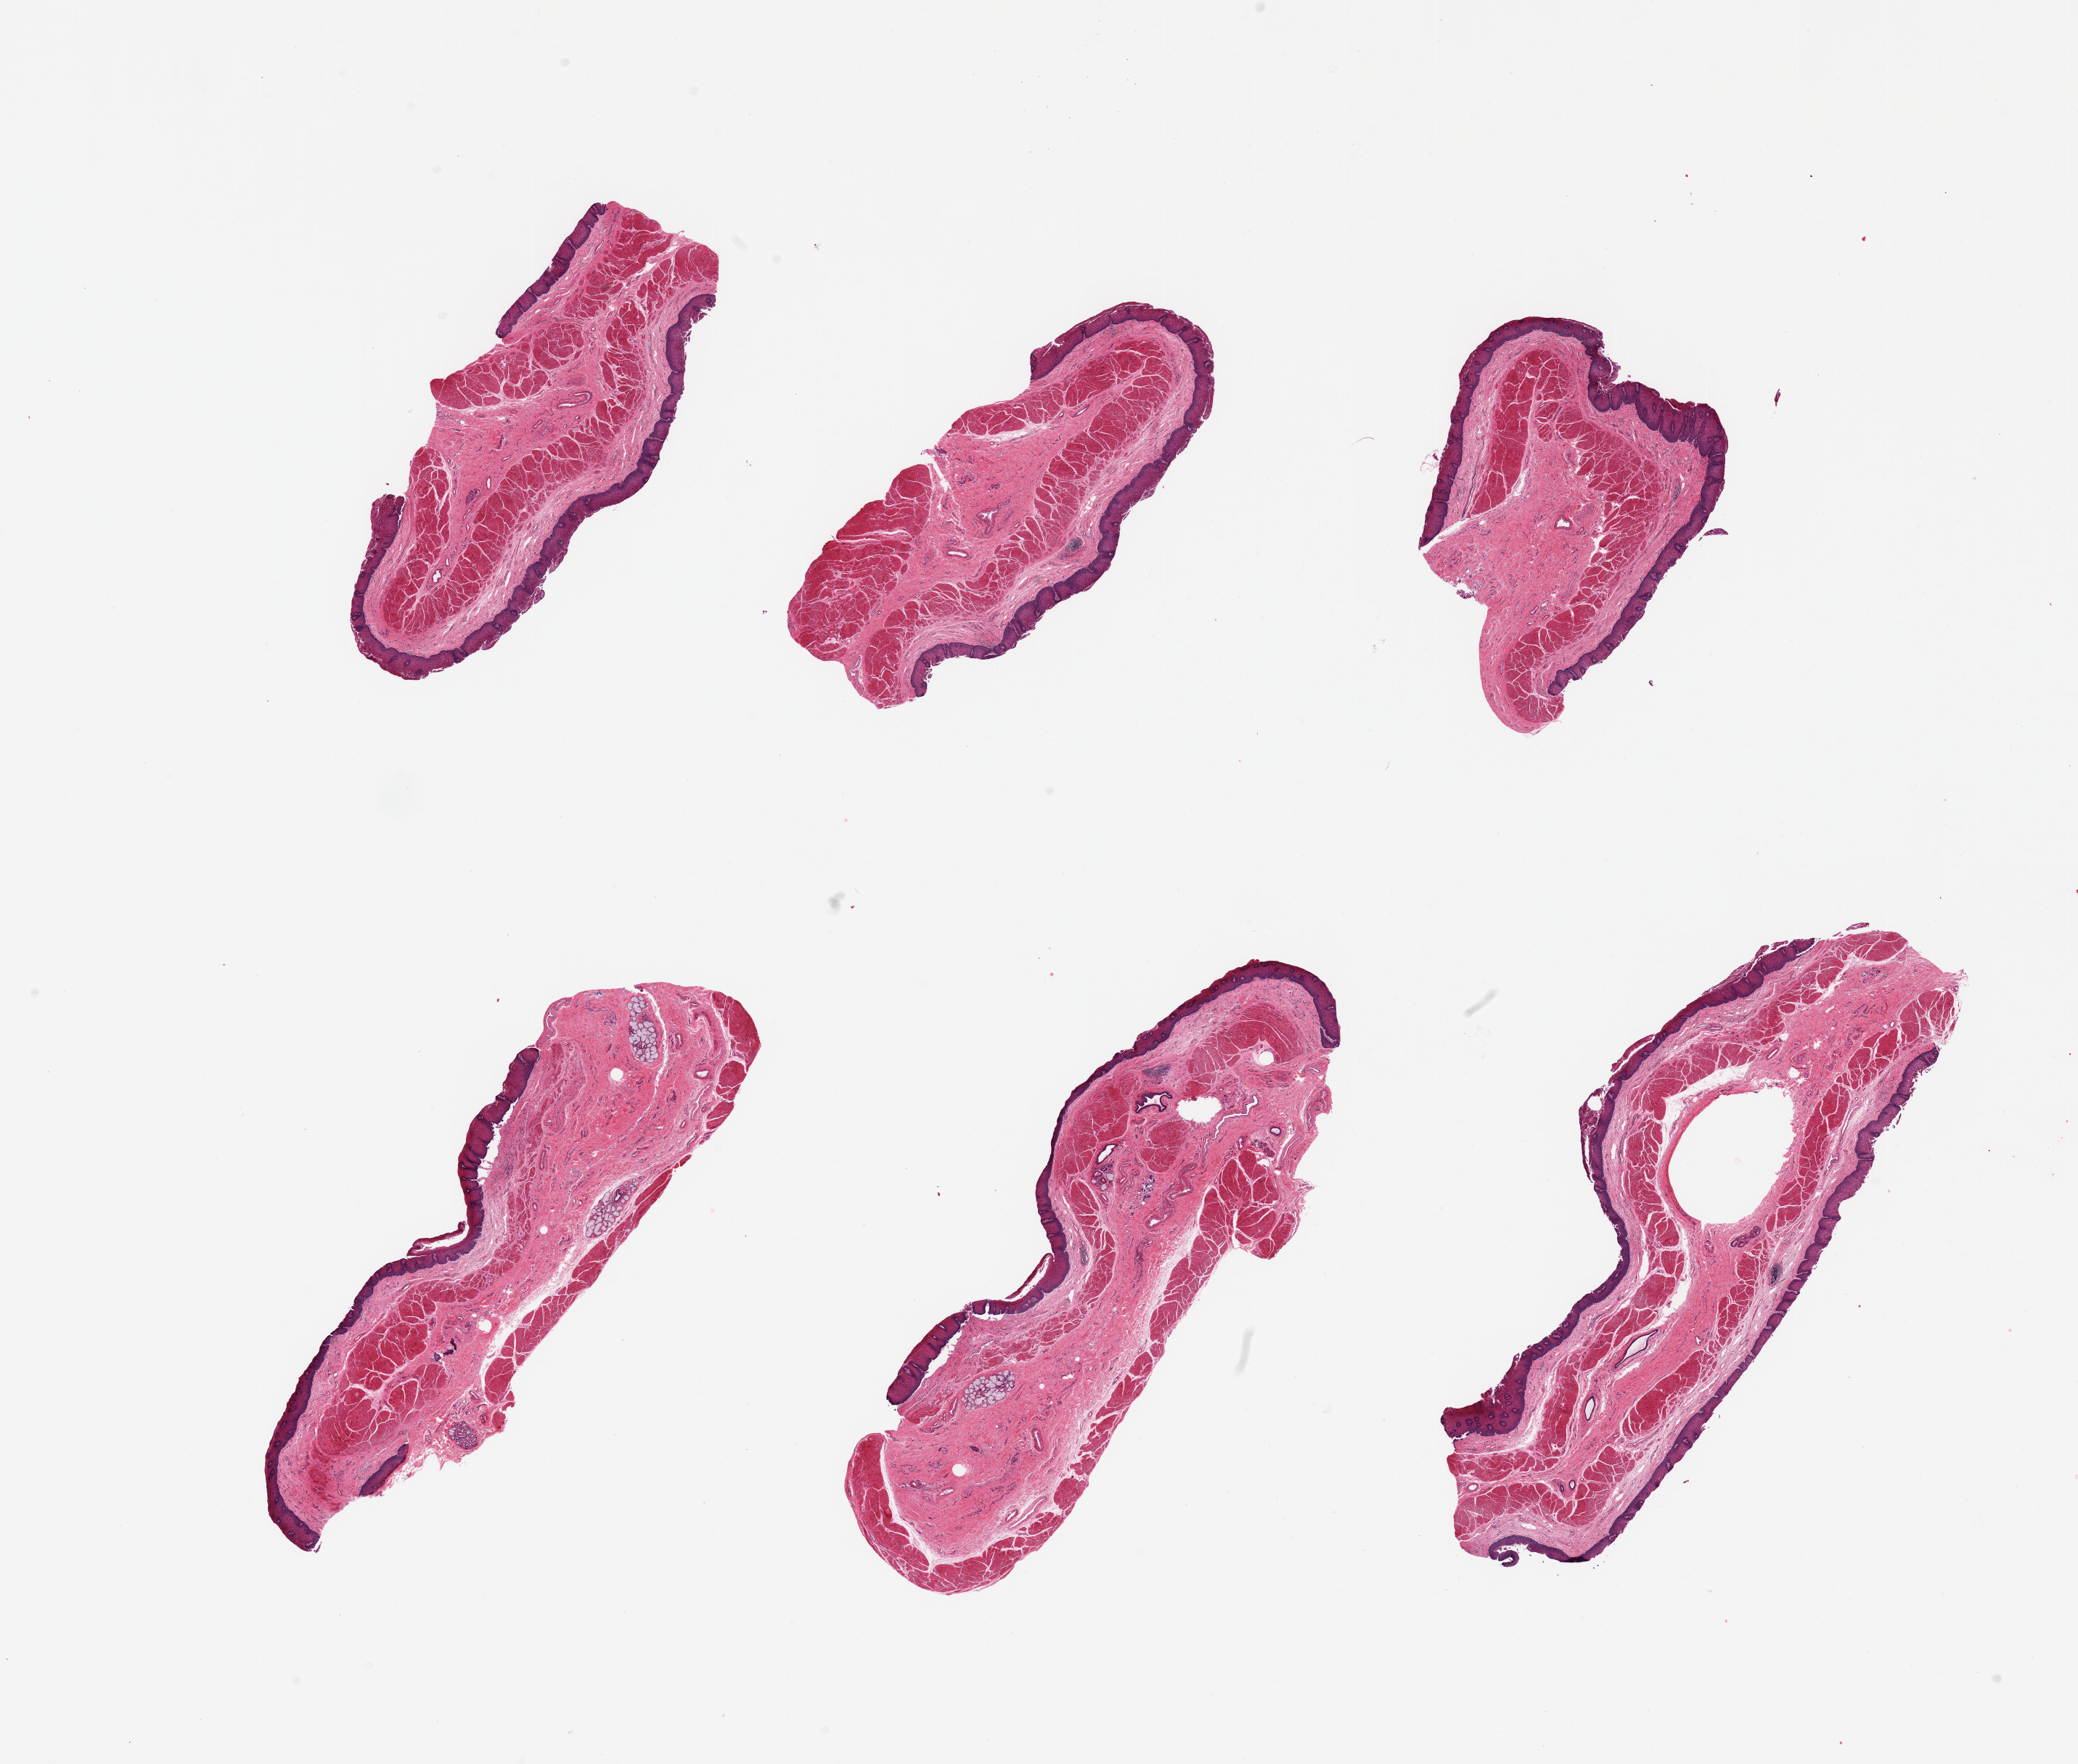
H&E whole-slide image, brightfield, a low-resolution overview of the entire scanned area, about 22.6 x 19.2 mm; PAXgene-fixed, paraffin-embedded tissue; sampled site (target tissue): esophageal mucous membrane; tissue donor sample. Donor sex: male.
Reviewer comment on this tissue sample: 6 pieces; only focal superficial desquamation; stratified squamous epithelium measures ~ 0.2mm in thickness; submucosal glands and dystrophic calcifications.